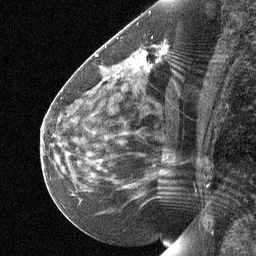
Breast MRI (dynamic contrast-enhanced), one sagittal slice. Dynamic contrast-enhanced study with each time point stored as its own series, time point 2 of 3 at this slice position (early post-contrast, ordered by acquisition time). 1.5 T. TE 4.8 ms, TR 27 ms. 2 mm slice thickness. 256 × 256 image matrix, field of view 180 × 180 mm. Patient: female, 51 years. Case-level facts recorded for this patient, not image findings: setting: breast cancer imaged before/during neoadjuvant chemotherapy; receptor status: HR-positive, HER2-negative.
Structures marked on this image (semi-automatically segmented with operator editing):
- analysis volume of interest (the breast-tissue region the enhancement analysis was run in; not a lesion): bounding box [x1, y1, x2, y2] px = [81, 35, 179, 103]
- tumour enhancement mask (voxels above the 90 % enhancement threshold inside the analysis volume of interest): [140, 54, 145, 56]